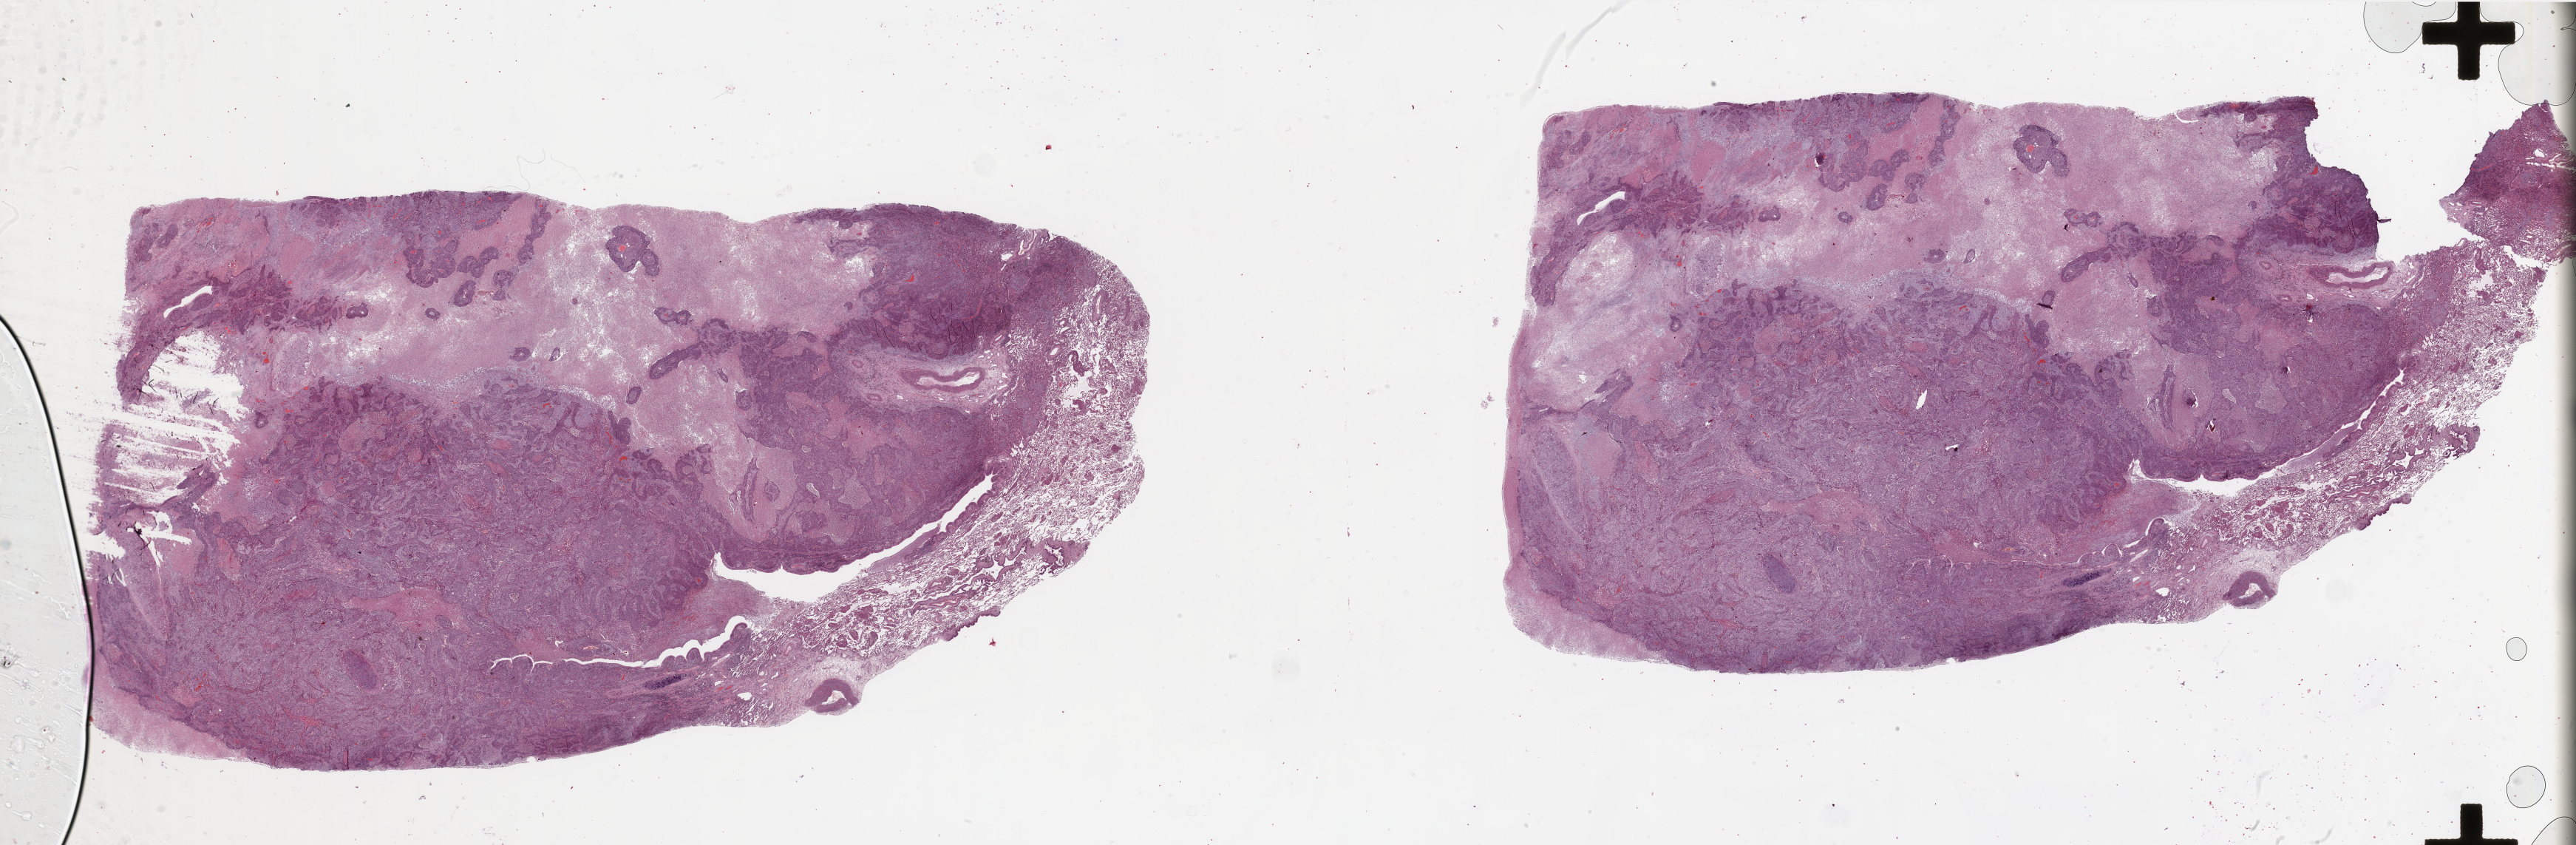
Whole-slide histology image, Hematoxylin and eosin (H&E) stained, a low-resolution overview of the entire scanned area, about 55.1 x 18.1 mm, lung, tumour tissue. 74-year-old male patient. Histologic grade: G2 (moderately differentiated).
- histologic diagnosis: Squamous cell carcinoma, NOS
- primary tumour site (as recorded): right middle lobe
- AJCC pathologic stage: IIA